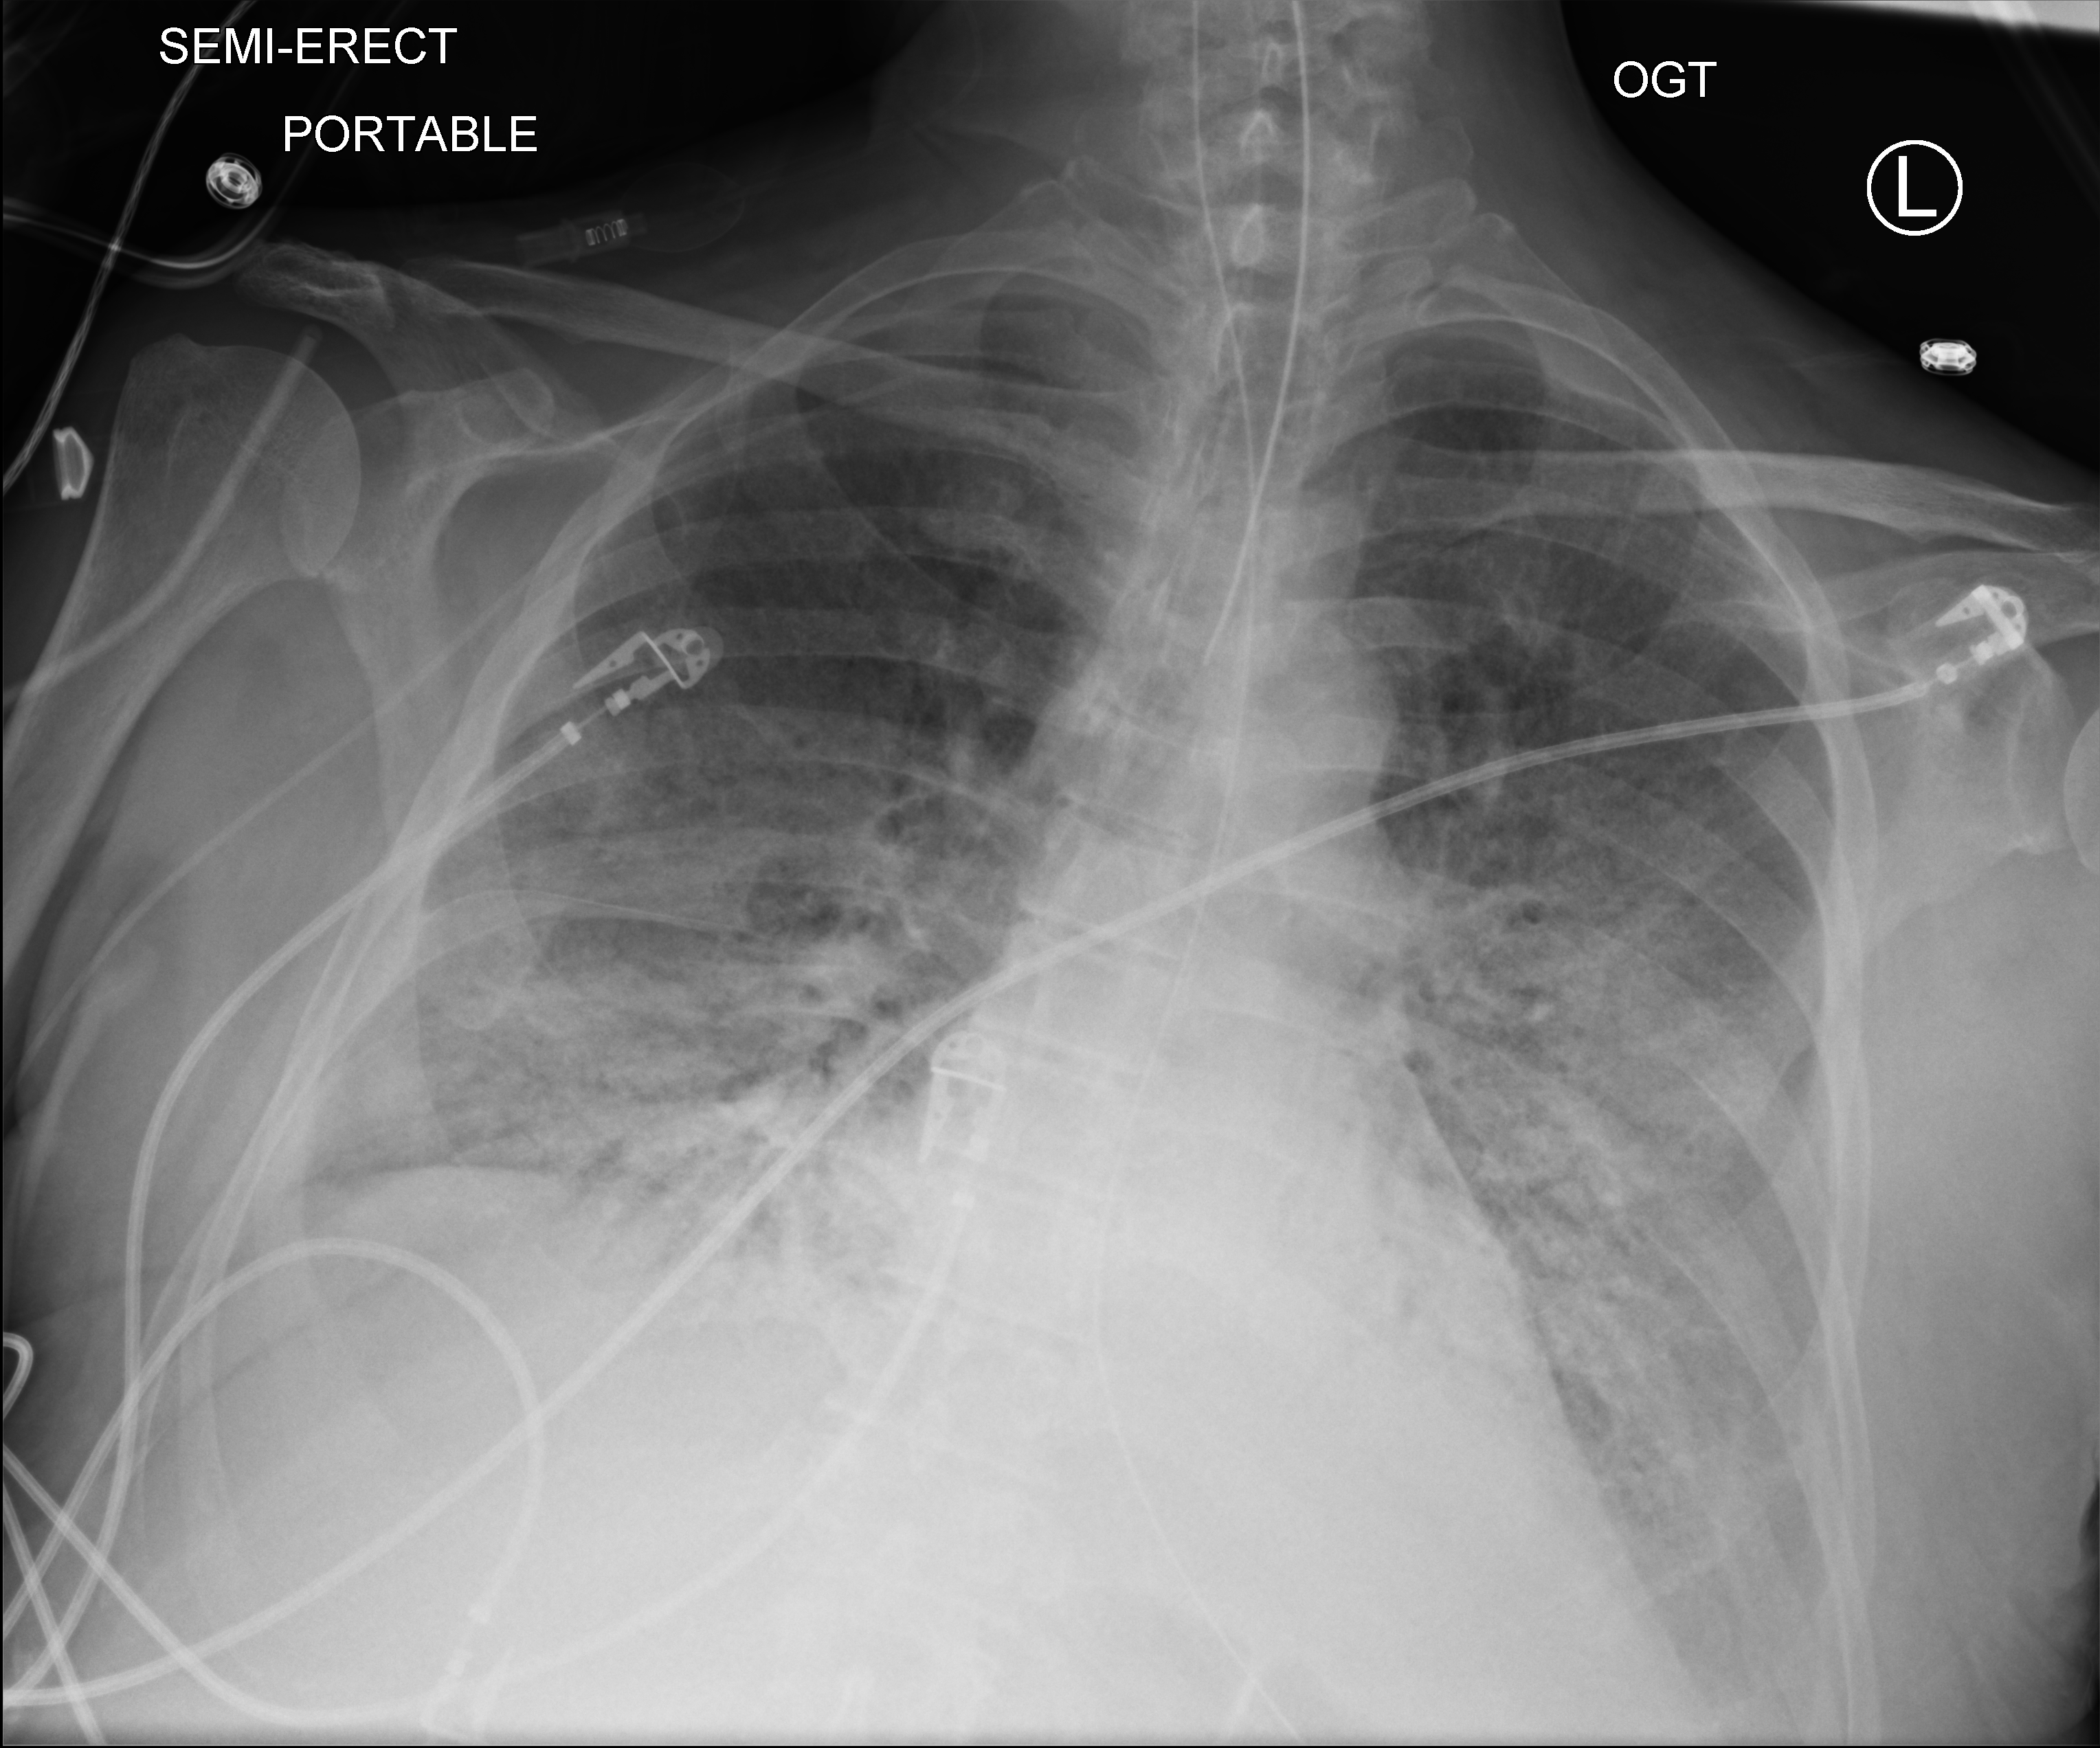
Chest X-ray (portable); anteroposterior (AP) projection. Male patient hospitalised with COVID-19, age 60–74 years.
Admission-level facts for this patient (not findings on this image; timing relative to this image not recorded):
- admitted to intensive care during this hospital stay: yes
- other chronic lung disease (admission record): no